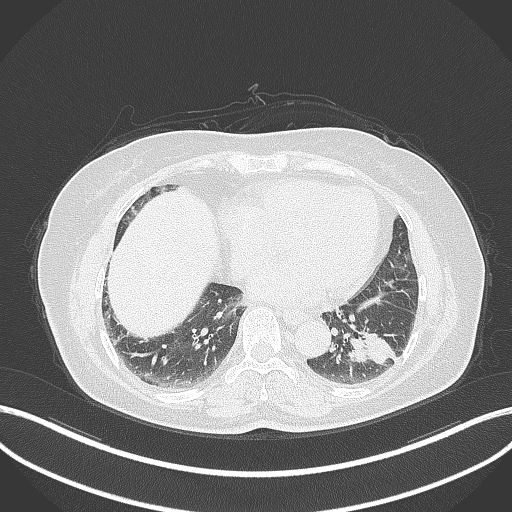
Chest CT, one axial slice. Slice 134 of 311 in the series (ordered by position). Reconstruction kernel B70f. Lung window (W 1500 / L -600 HU). 1 mm slice thickness. 512 × 512 image matrix. Patient: female, 59 years. Case-level facts recorded for this patient, not image findings: clinical TNM (as recorded): T2a N0 M0.
Annotated regions visible in this slice (bounding box drawn by a radiologist):
- lung tumour (recorded histology: adenocarcinoma): bounding box (x1, y1, x2, y2) in pixels: (345, 325, 400, 369)